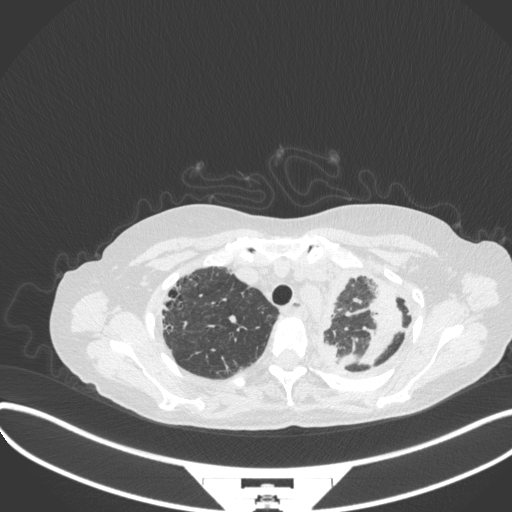
Chest CT, one axial slice; slice 279 of 373 in the series (ordered by position); 120 kVp; lung window (W 1500 / L -600 HU); 1 mm slice thickness; 512 × 512 image matrix, field of view 400 × 400 mm. Female patient, age 56 years. From the clinical record (not read from this slice): clinical TNM (as recorded): T1 N0 M0.
Annotated regions visible in this slice (bounding box drawn by a radiologist):
- lung tumour (recorded histology: adenocarcinoma): box from (x=349, y=283) to (x=405, y=365) px